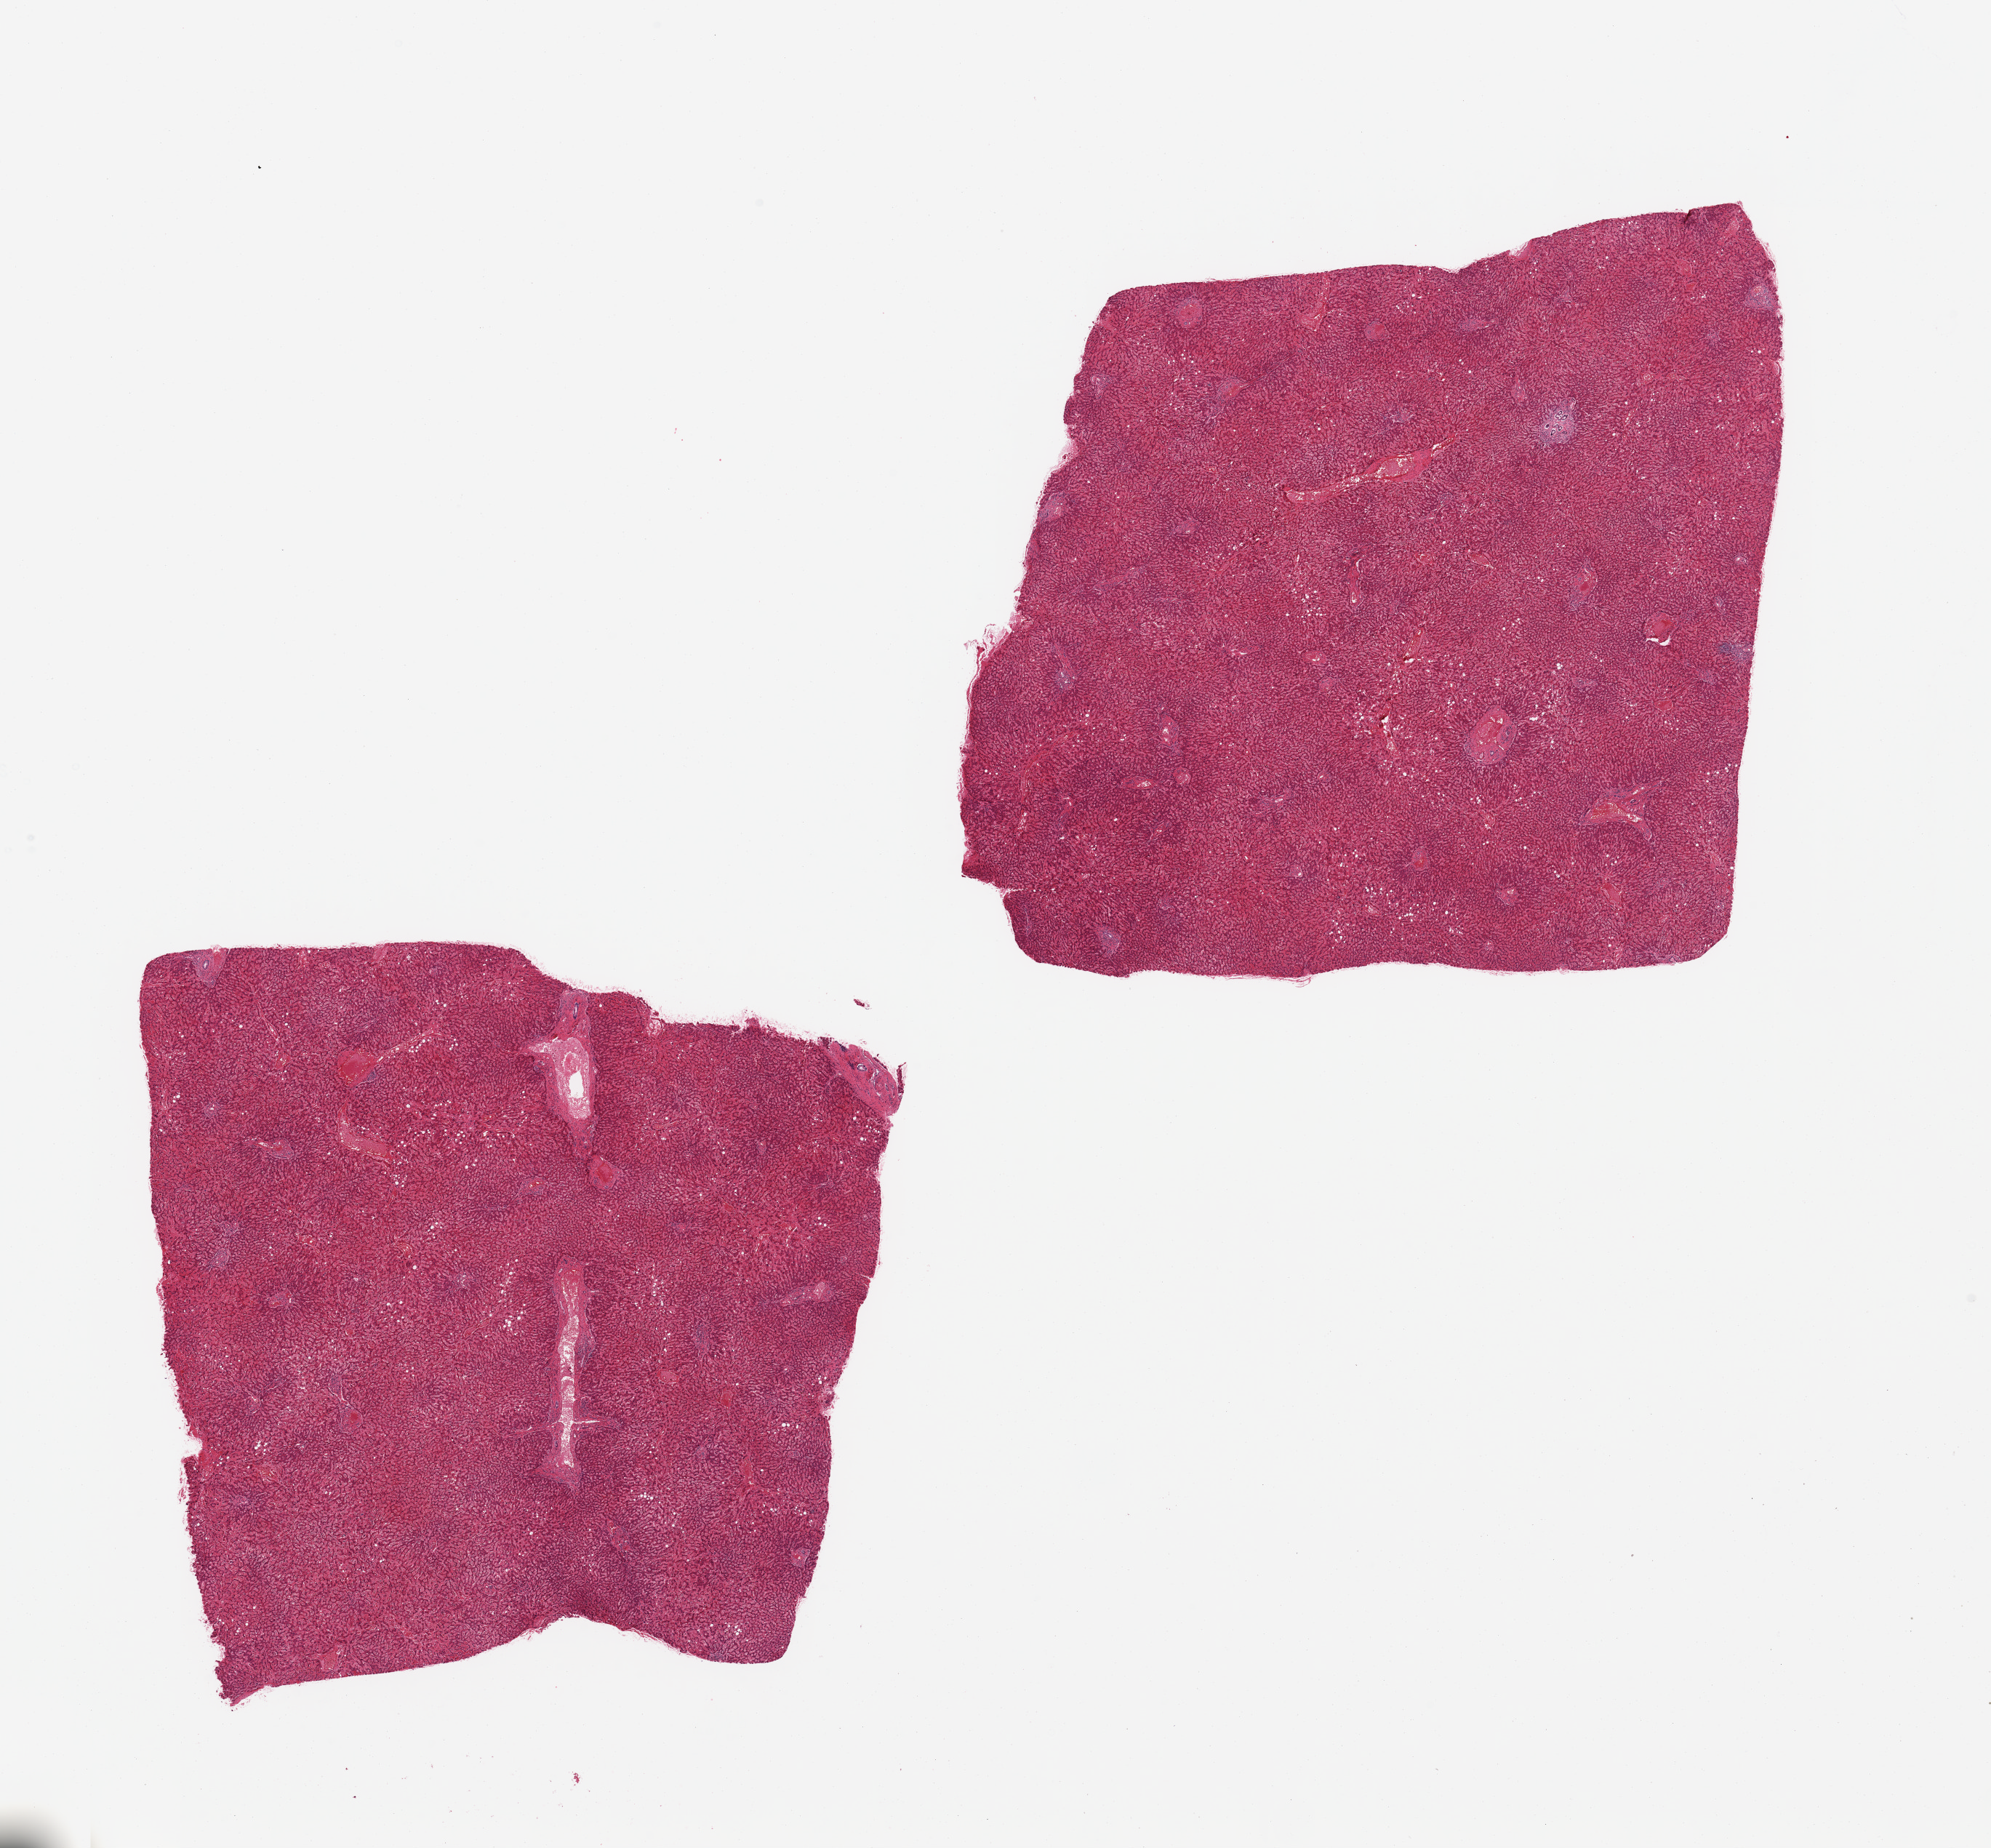
Digitized H&E-stained section — whole scanned area (about 21.7 x 20.1 mm, acquisition: 20x scan) shown as a low-resolution overview, PAXgene-fixed, paraffin-embedded tissue, target tissue: liver, tissue donor sample. Donor: male.
Review note (as recorded): 2 pieces, minimal macrovesicular steatosis (~10% of parenchyma), moderate passive congestion.